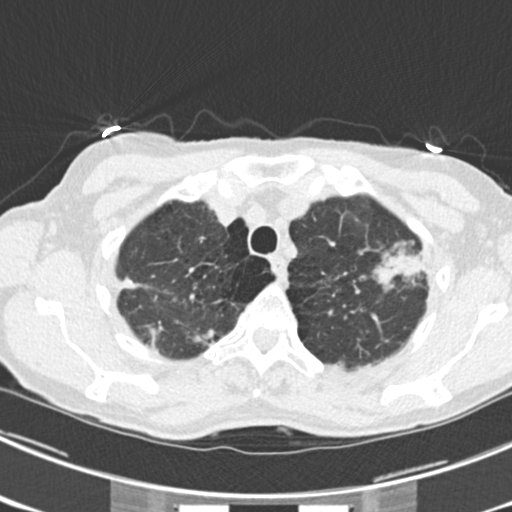
Low-dose screening chest CT, one axial slice. Slice 184 of 225 in the series (ordered by position). Lung window (W 1500 / L -600 HU). 512 × 512 image matrix, field of view 302 × 302 mm.
Annotated regions visible in this slice (manually delineated by an expert):
- lesion 1 (tumor, upper lobe of left lung): box from (x=376, y=252) to (x=424, y=285) px